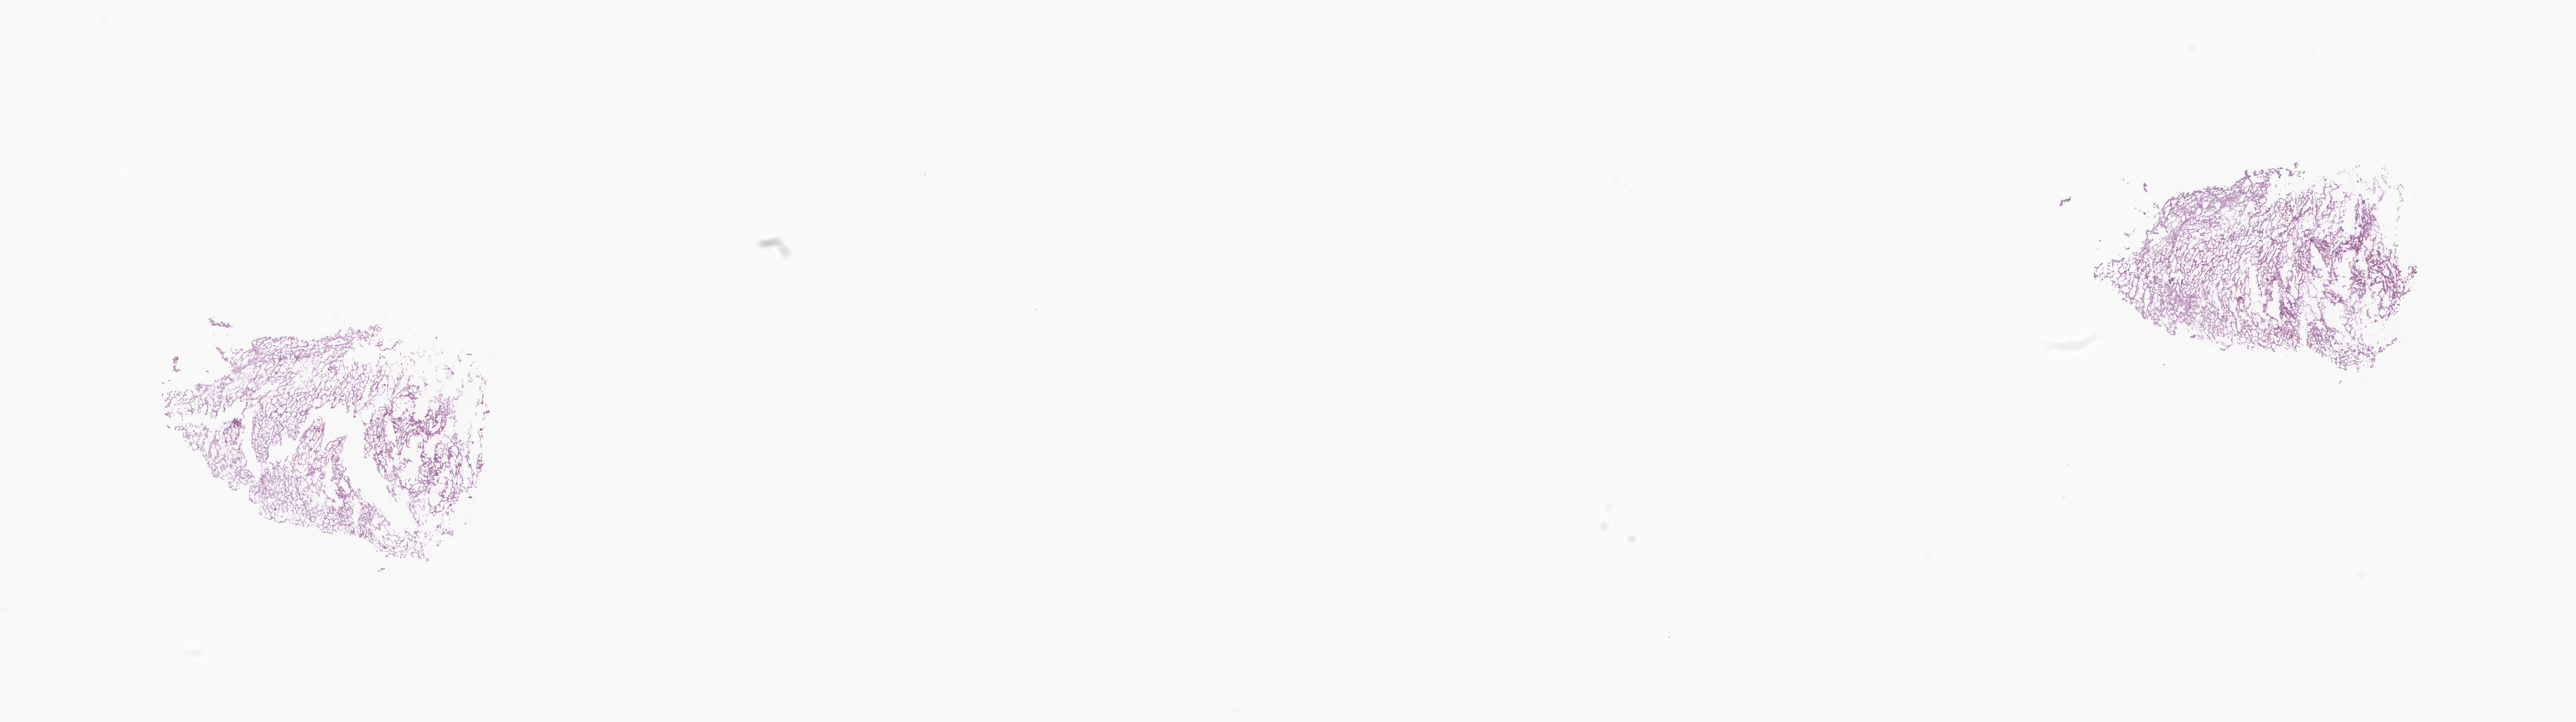
Digitized haematoxylin and eosin-stained section of tumor tissue from the cerebellum — a low-resolution overview of the entire scanned area, about 29.8 x 8.4 mm; frozen section (OCT-embedded). Patient: male, age 98 months (8 years 2 months).
Diagnosis: Glioma, malignant.